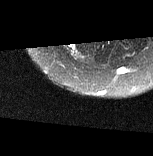
MRI of an extremity soft-tissue mass, one axial slice. Position 11 of 77 along the scan axis. T2-weighted fat-saturated. MR volume resampled by the dataset authors to the PET/CT grid (not the native acquisition matrix). 3.27 mm slice thickness. 153 × 156 image matrix. Female patient. From the clinical record (not read from this slice): histological type: synovial sarcoma; grade: intermediate; site of the primary tumour: right buttock.
Outlined on this slice (expert contour drawn on MRI and transferred to this co-registered scan by the dataset authors):
- gross tumour volume including surrounding oedema: bounding box <67,43,77,55> (left, top, right, bottom; pixels)